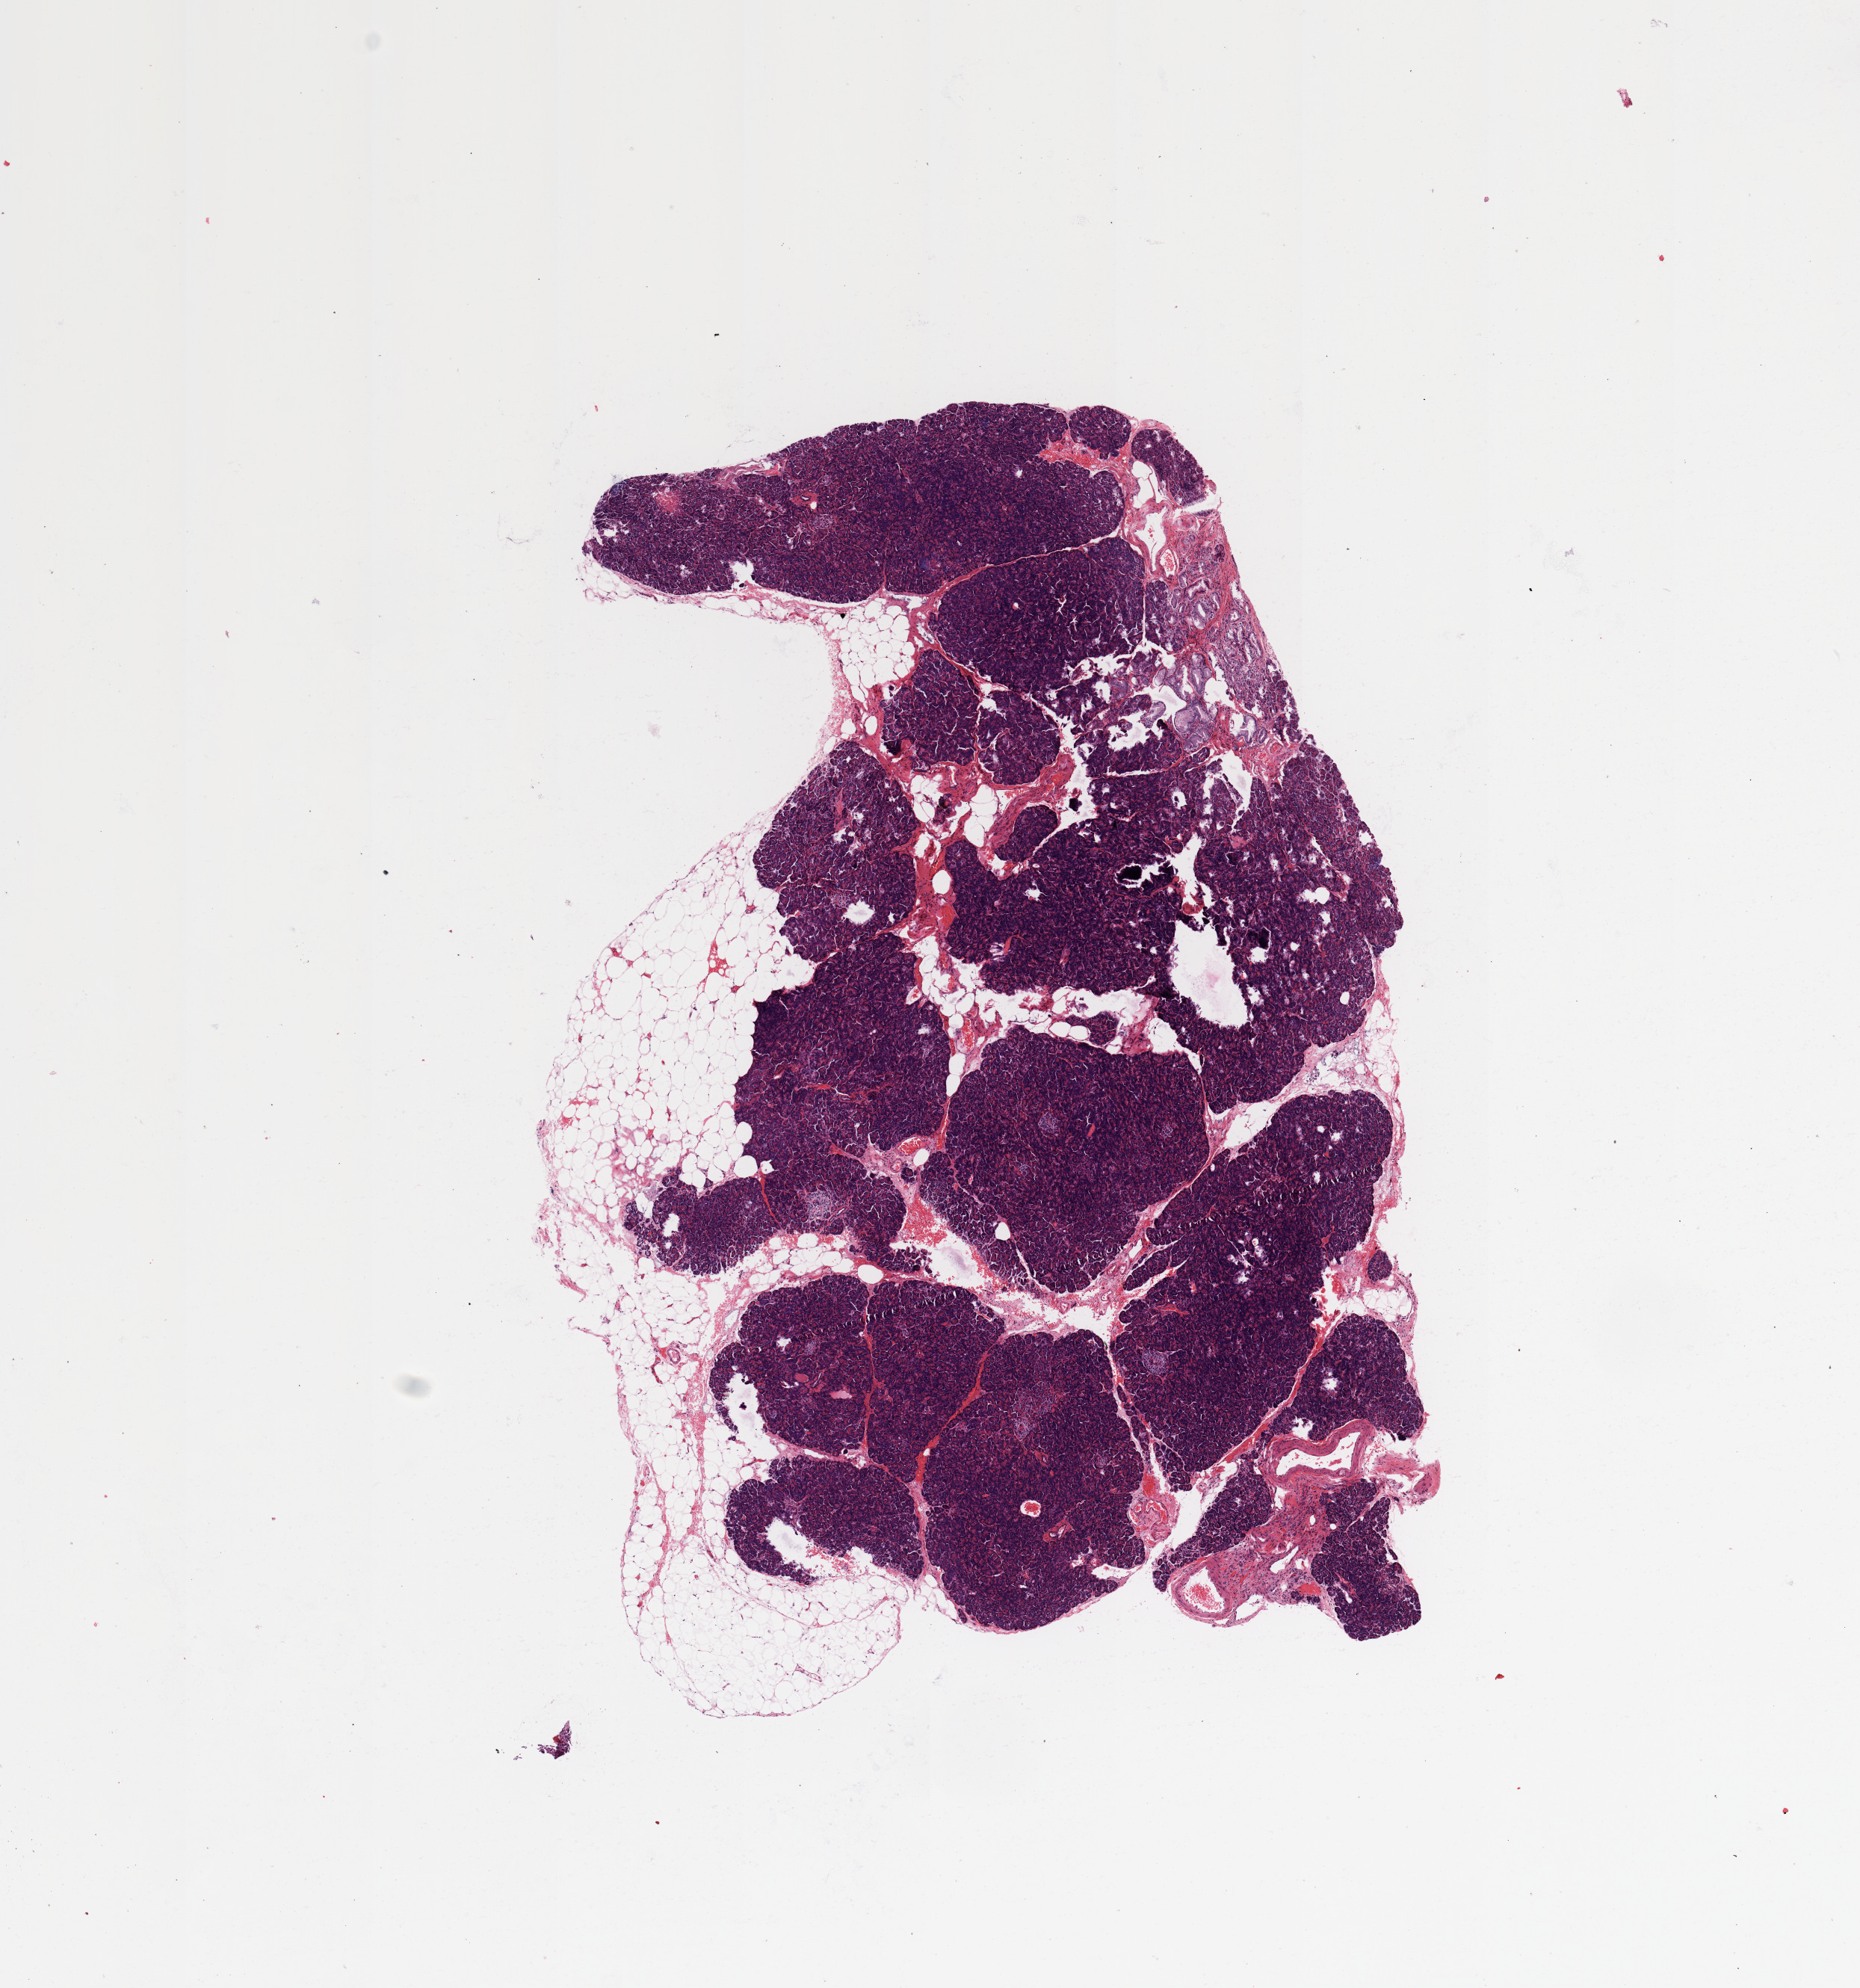
Digitized H&E-stained tissue section (whole slide), low-resolution overview of the scanned area, about 9.8 x 10.5 mm, pancreas, normal (non-tumour) tissue. 62-year-old female patient.
This section: normal (non-tumour) tissue from the same patient. Patient diagnosis: Infiltrating duct carcinoma, NOS.